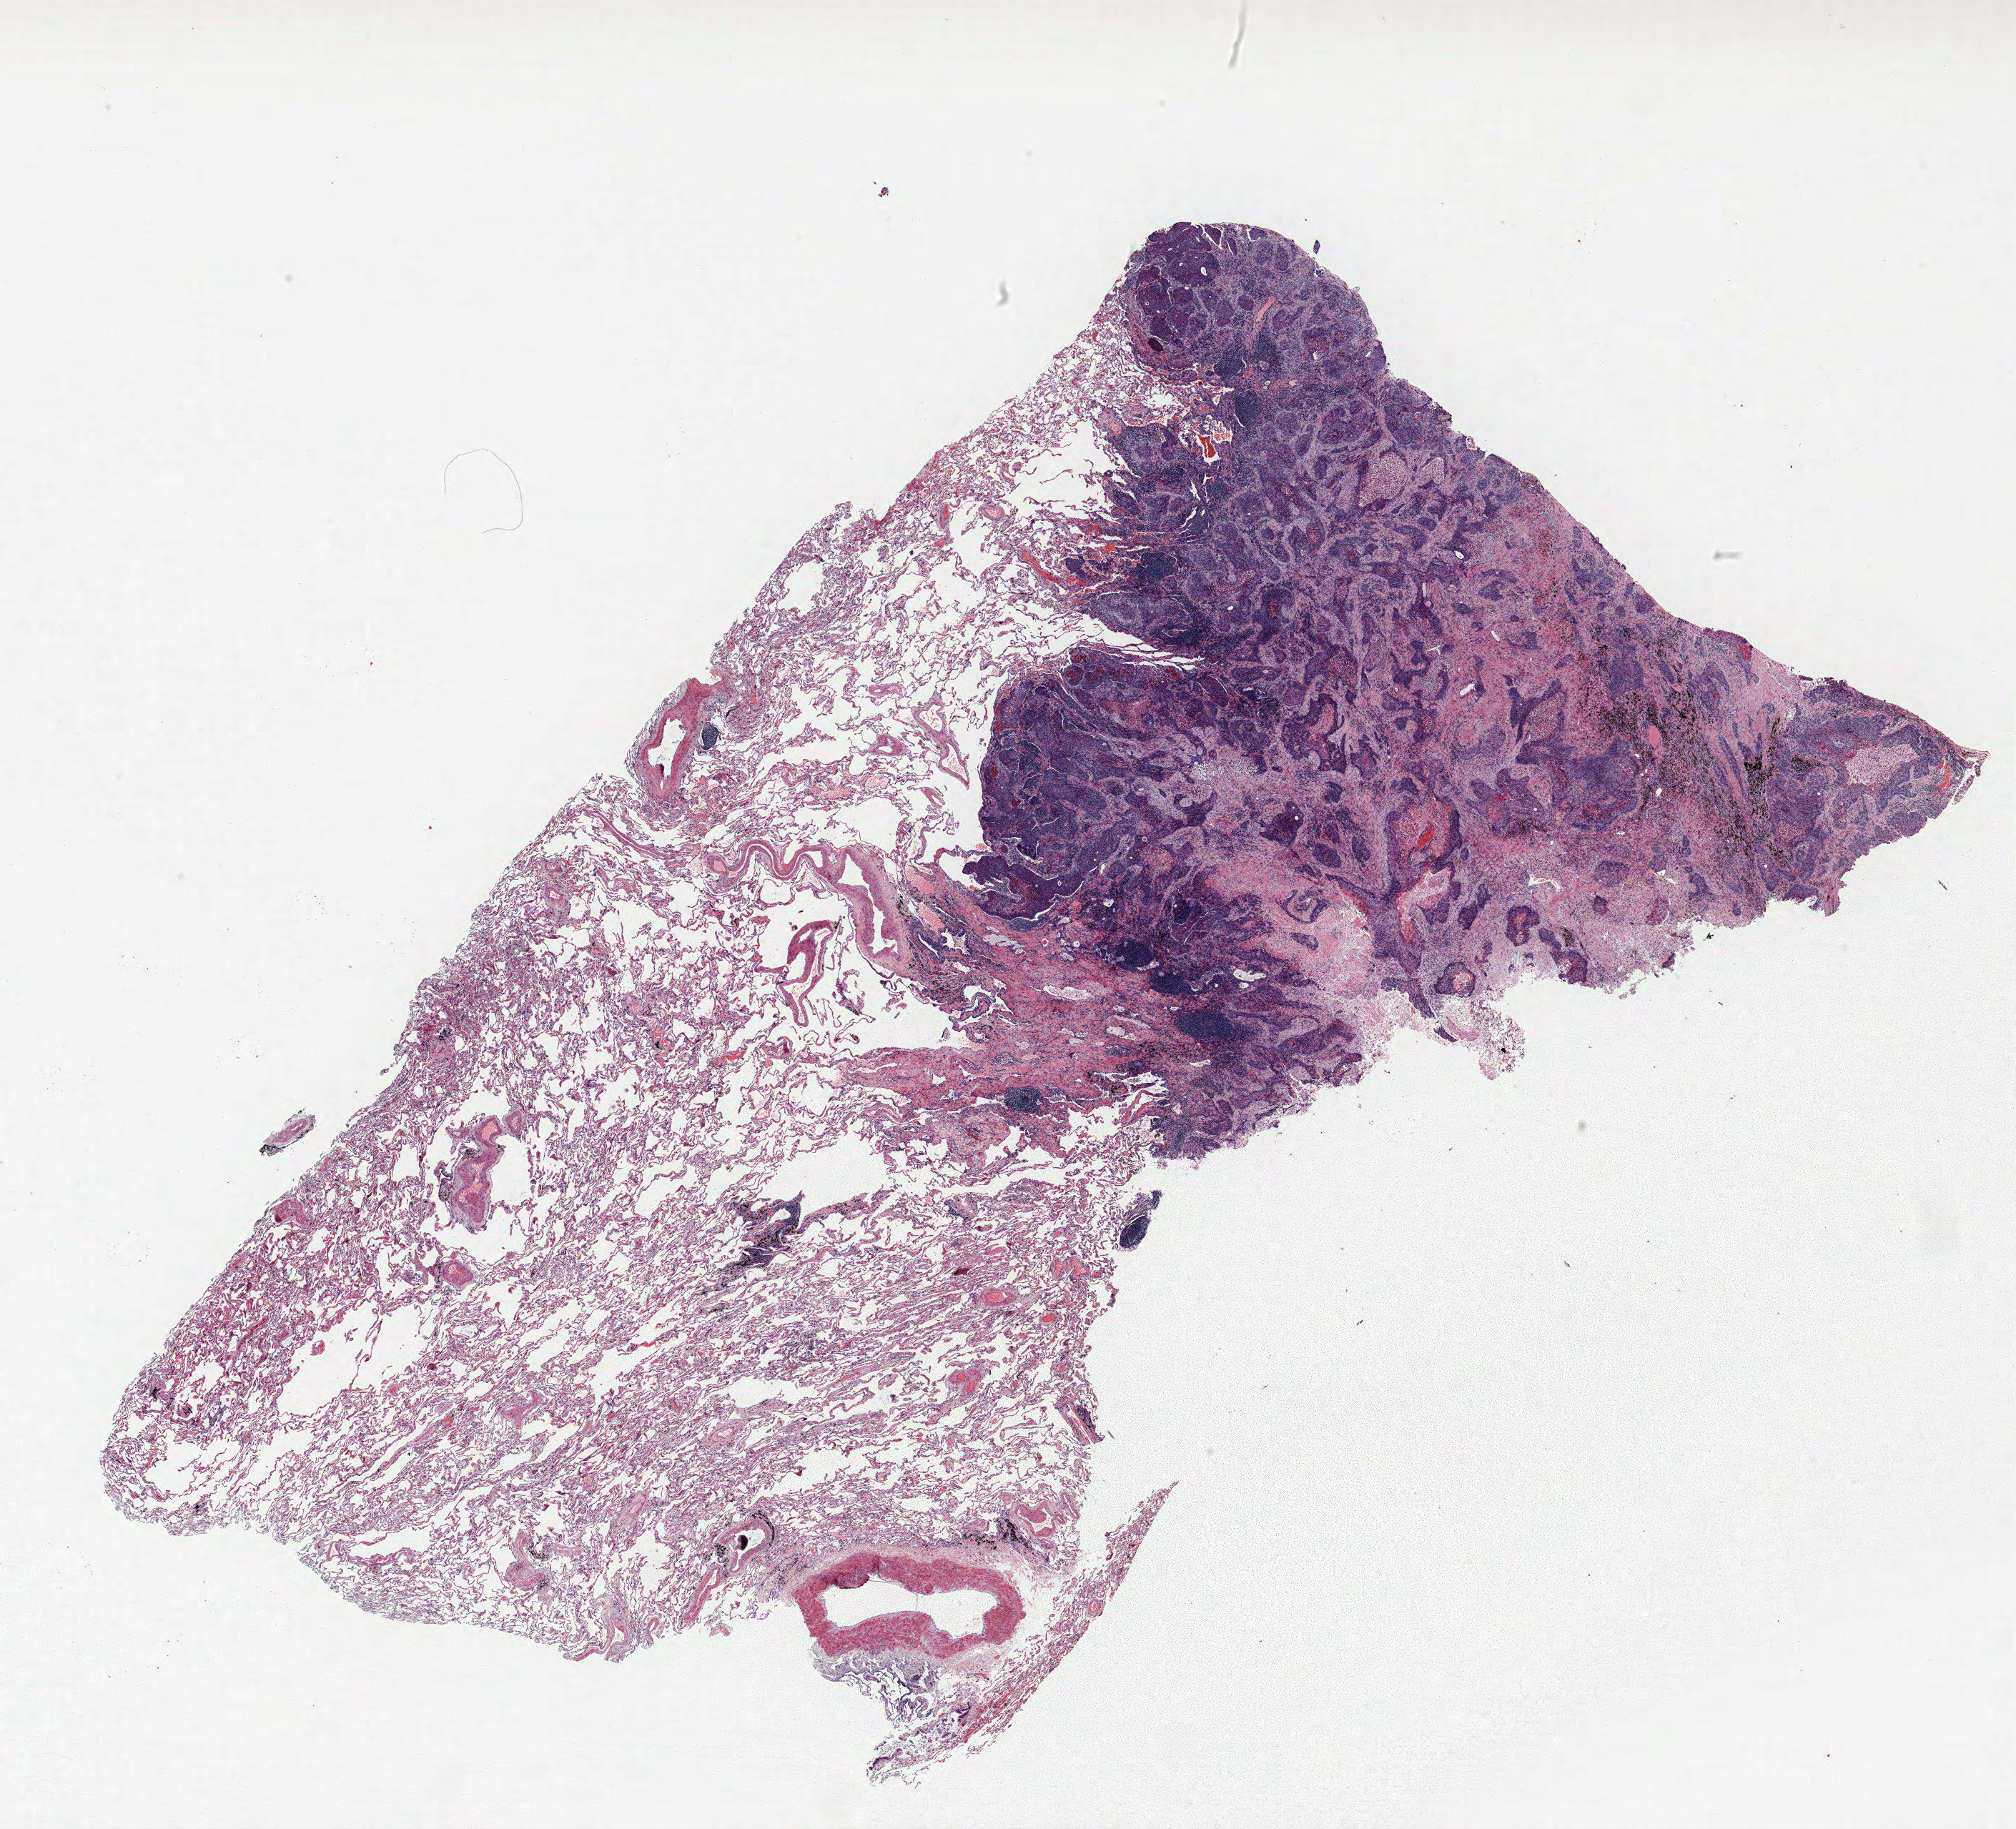
Hematoxylin and eosin (H&E) stained whole-slide image, whole scanned area (about 22.6 x 20.5 mm, acquisition: 40x scan) shown as a low-resolution overview; formalin-fixed paraffin-embedded (FFPE) section; lung. Male patient, aged 70 at enrolment. Former smoker at enrolment. Grade: poorly differentiated (G3).
Participant's lung-cancer diagnosis: Squamous cell carcinoma, NOS (ICD-O-3 8070/3). Primary tumour location (clinical record): right upper lobe. Stage (AJCC 6th edition): IA. Tumour size (pathology): 18 mm.